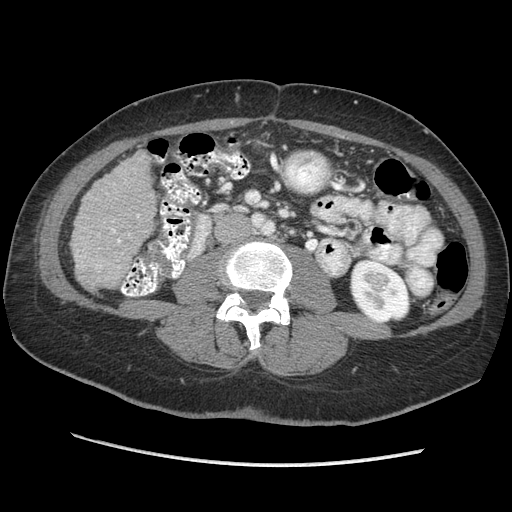
Contrast-enhanced abdominal CT (liver protocol), one axial slice; slice 93 of 170 in the series (ordered by position); reconstruction kernel STANDARD; 140 kVp; soft-tissue window (W 400 / L 40 HU); 512 × 512 image matrix, field of view 360 × 360 mm. Case-level facts recorded for this patient, not image findings: diagnosis: hepatocellular carcinoma (patient treated with transarterial chemoembolisation; whether this scan precedes or follows treatment is not stated here); TNM stage (as recorded): Stage-II; Child-Pugh class: A; tumour differentiation: no biopsy; tumour nodularity: multinodular.
Outlined on this slice (semi-automatic segmentation, software-assisted and operator-edited):
- liver parenchyma outside the tumour (the mass and vessels are separate outlines, so this box may not span the whole liver): bounding box [x1, y1, x2, y2] px = [70, 150, 156, 286]
- liver vessels: [100, 215, 140, 267]